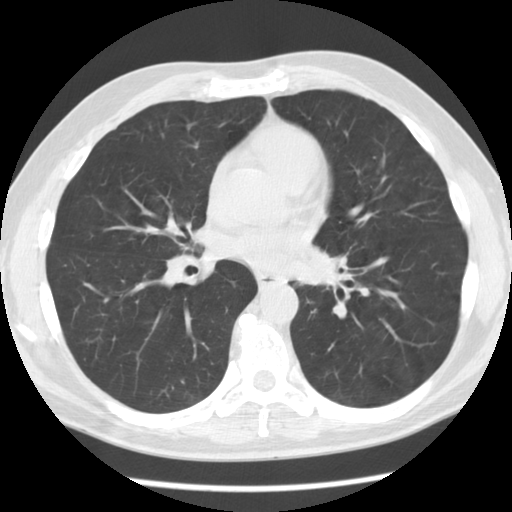
Chest CT (low-dose screening protocol), one axial image. Baseline annual screen. Lung window (W 1500 / L -600 HU). 2.5 mm slice thickness. 120 kVp. Slice 61 of 112 in the series. Male participant, aged 55 years at enrolment.
• Lesion marked by an expert reader, bounding box <279,235,349,307> (left, top, right, bottom; pixels).
• Screening reader's record for this exam: no non-calcified nodule ≥4 mm recorded.
• Lung cancer was diagnosed 223 days after this screen: squamous cell carcinoma, NOS, left lower lobe, moderately differentiated (G2), stage IV (AJCC 6th edition), 51 mm at pathology.